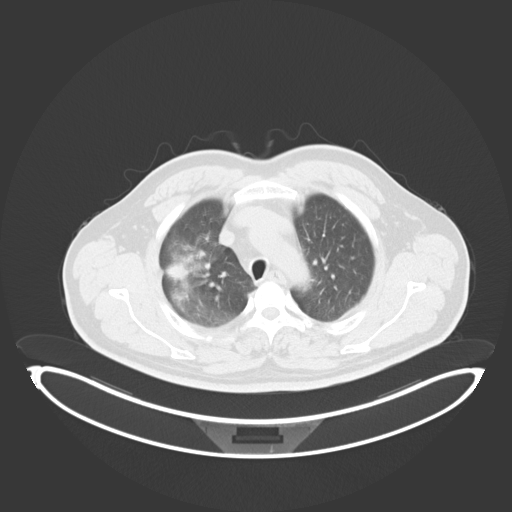
Chest CT, one axial slice; slice 227 of 284 in the series (ordered by position); 120 kVp; lung window (W 1500 / L -600 HU); 512 × 512 image matrix, field of view 500 × 500 mm. Male patient, age 55 years. From the clinical record (not read from this slice): clinical TNM (as recorded): T3 N2 M1.
Outlined on this slice (rectangle marked by the reading radiologist):
- lung tumour (recorded histology: adenocarcinoma): bounding box <165,243,200,301> (left, top, right, bottom; pixels)